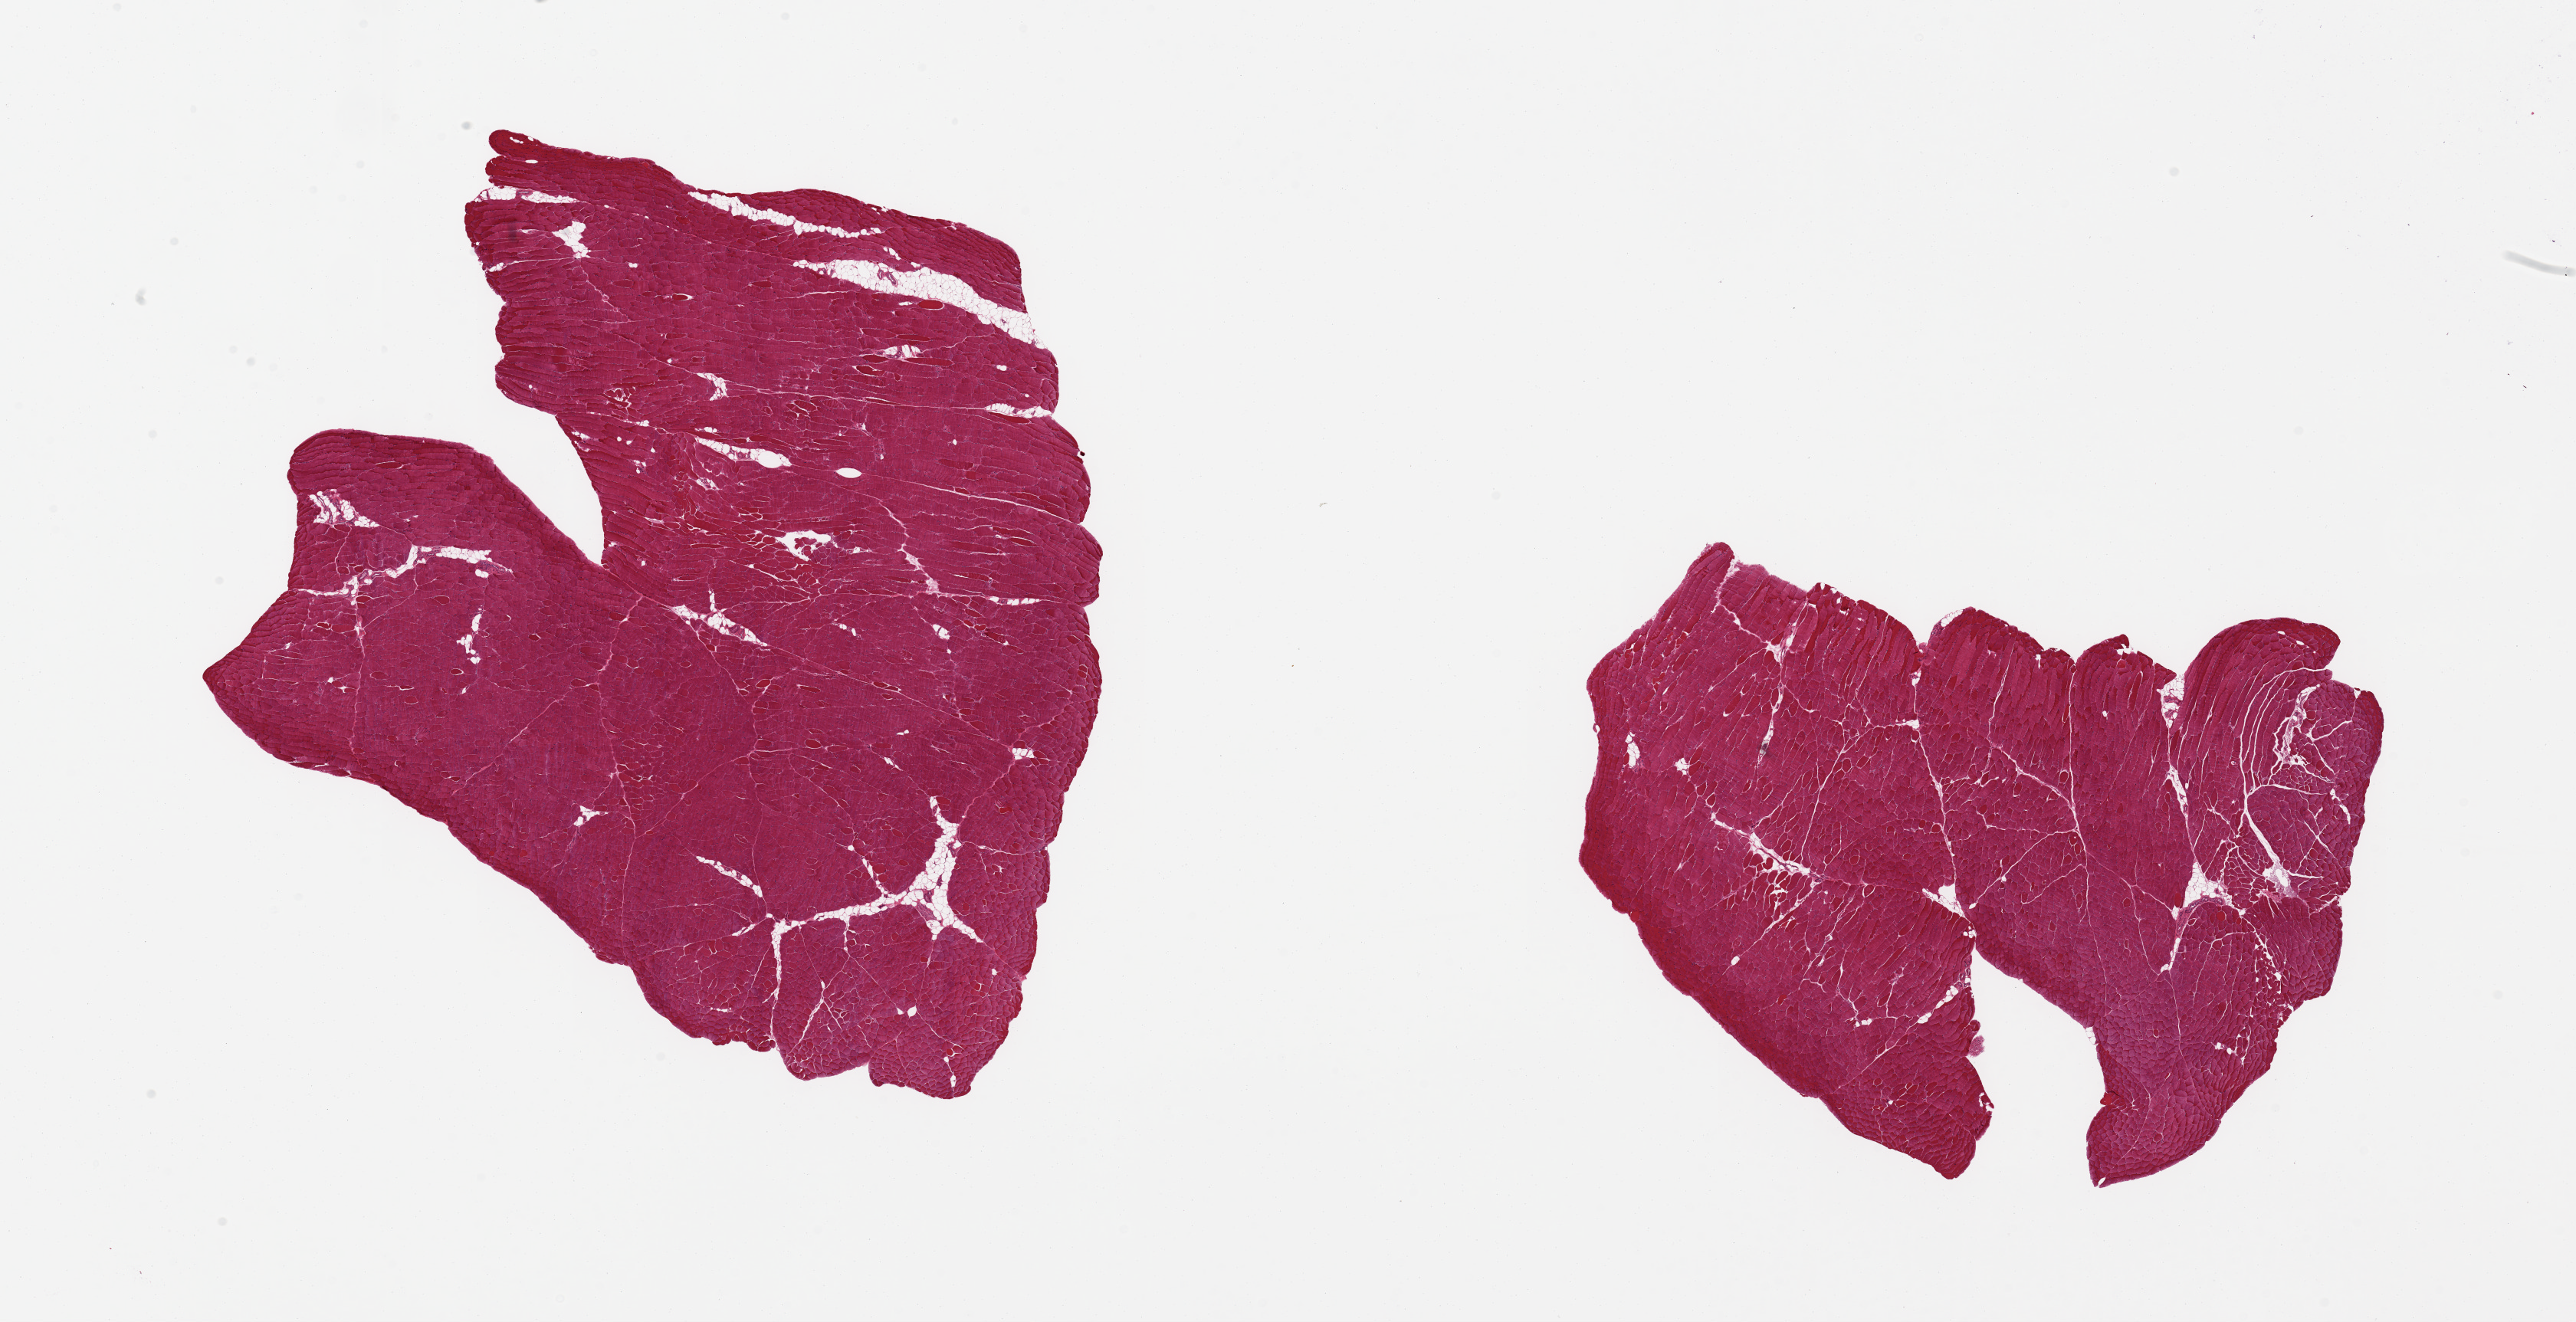
Hematoxylin and eosin (H&E) whole-slide image, brightfield — a low-resolution overview of the entire scanned area, about 26.6 x 13.6 mm (acquisition: 20x scan), PAXgene-fixed, paraffin-embedded tissue, target tissue: skeletal muscle, tissue donor sample. Donor: female.
* reviewer comment on this tissue sample: 2 pieces